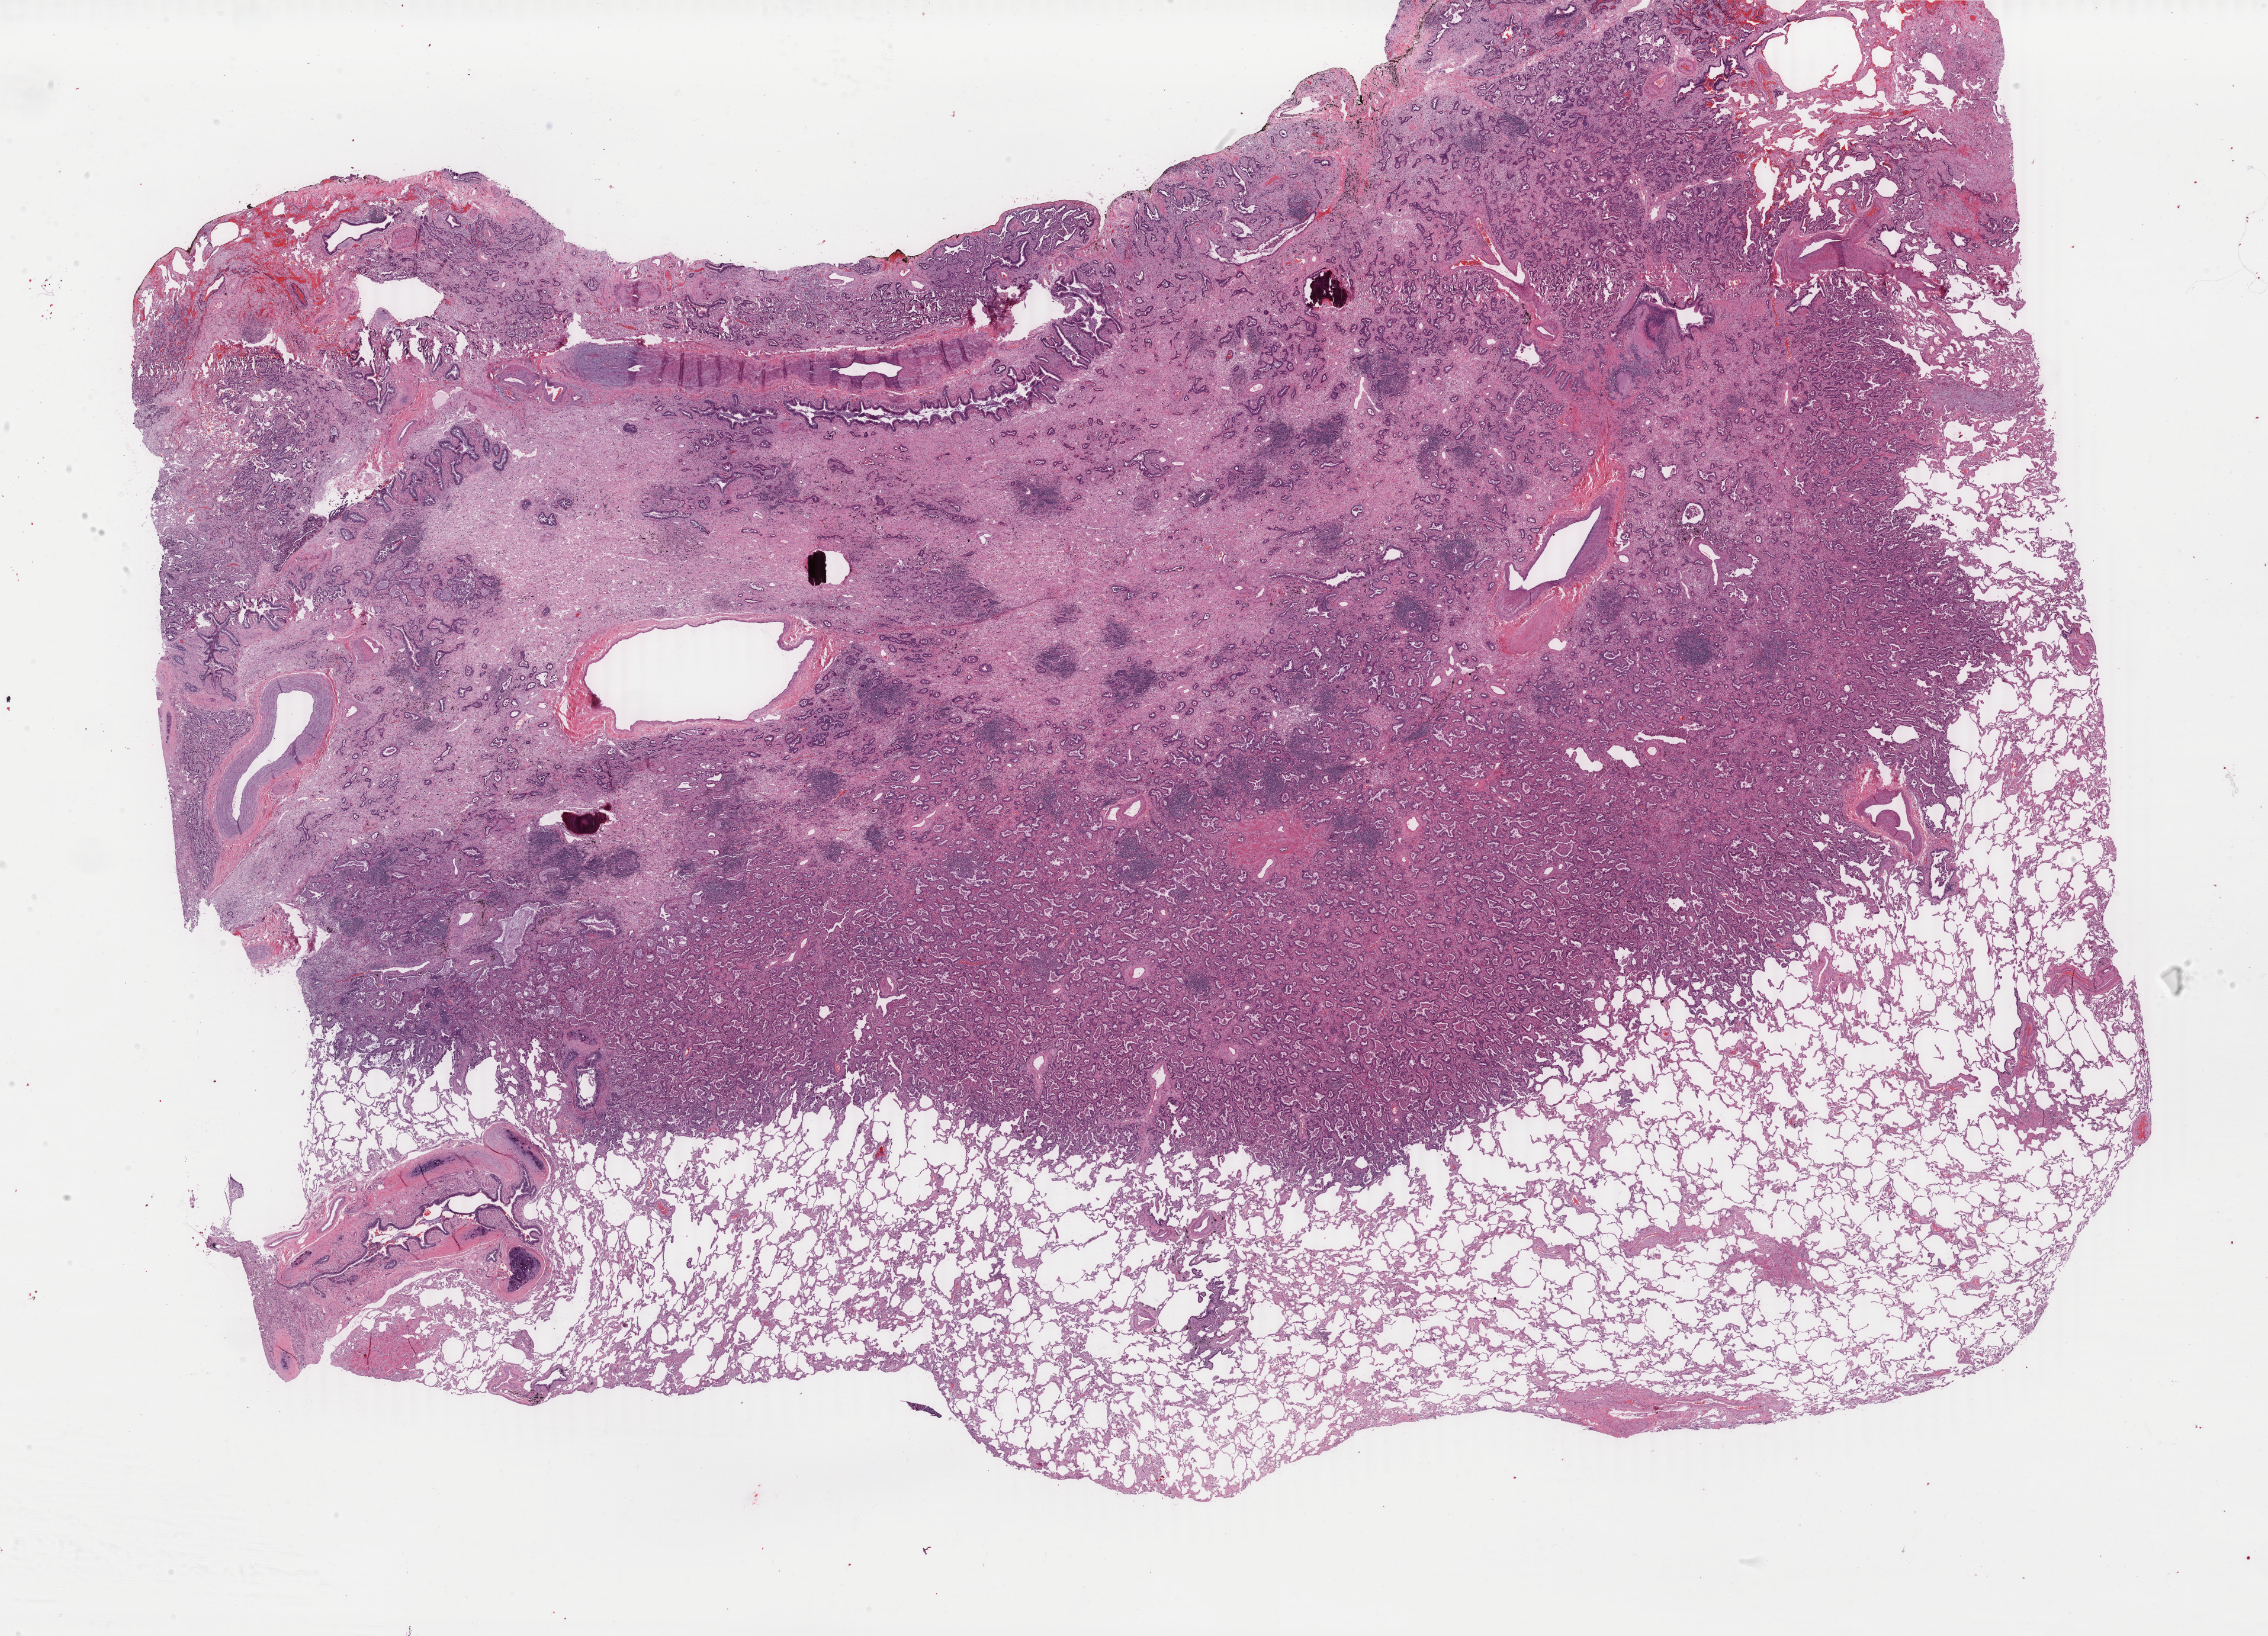
Digitized H&E-stained tissue section (whole slide) — whole scanned area (about 30.5 x 22.0 mm, slide scanned at 40x) shown as a low-resolution overview. Formalin-fixed paraffin-embedded (FFPE) diagnostic section. Sample: primary tumour, lung. Female patient; age at initial diagnosis 75 years.
Diagnosis: Acinar cell carcinoma (upper lobe, lung). AJCC pathologic stage: IB (7th edition). Laterality: right.